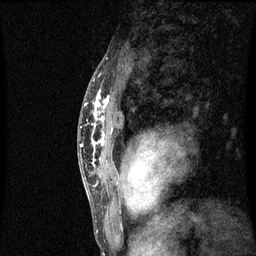
Breast MRI (dynamic contrast-enhanced), one sagittal slice. Position 45 of 60 along the scan axis. Dynamic contrast-enhanced series, image 2 of 3 at this slice position (ordered by acquisition). 1.5 T. TE 4.2 ms, TR 8.9 ms. 256 × 256 image matrix. Female patient, age 50 years. From the clinical record (not read from this slice): setting: breast cancer imaged before/during neoadjuvant chemotherapy; receptor status: triple-negative.
Structures marked on this image (semi-automatic segmentation, software-assisted and operator-edited):
- analysis volume of interest (the breast-tissue region the enhancement analysis was run in; not a lesion): bounding box (x1, y1, x2, y2) in pixels: (84, 80, 117, 171)
- tumour enhancement mask (voxels above the 70 % enhancement threshold inside the analysis volume of interest): (86, 90, 111, 145)